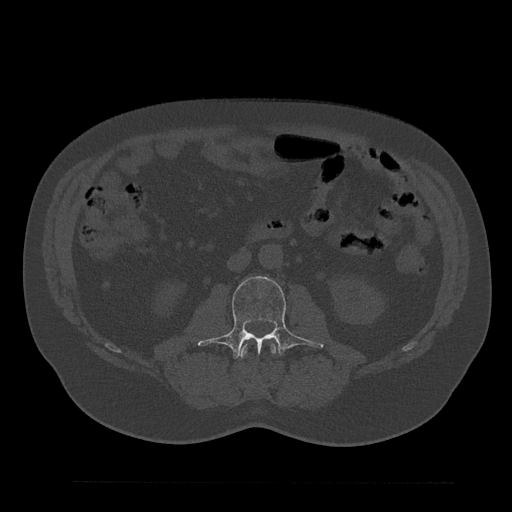
CT including the spine, one axial slice. Position 46 of 797 along the scan axis. Bone window (W 1800 / L 400 HU). 0.5 mm slice thickness. 512 × 512 image matrix. Male patient, age 61 years. From the clinical record (not read from this slice): primary cancer: prostate.
Outlined on this slice (semi-automatically segmented with operator editing):
- L2 vertebra: bounding box <240,344,276,383> (left, top, right, bottom; pixels)
- L3 vertebra: <198,276,323,359>